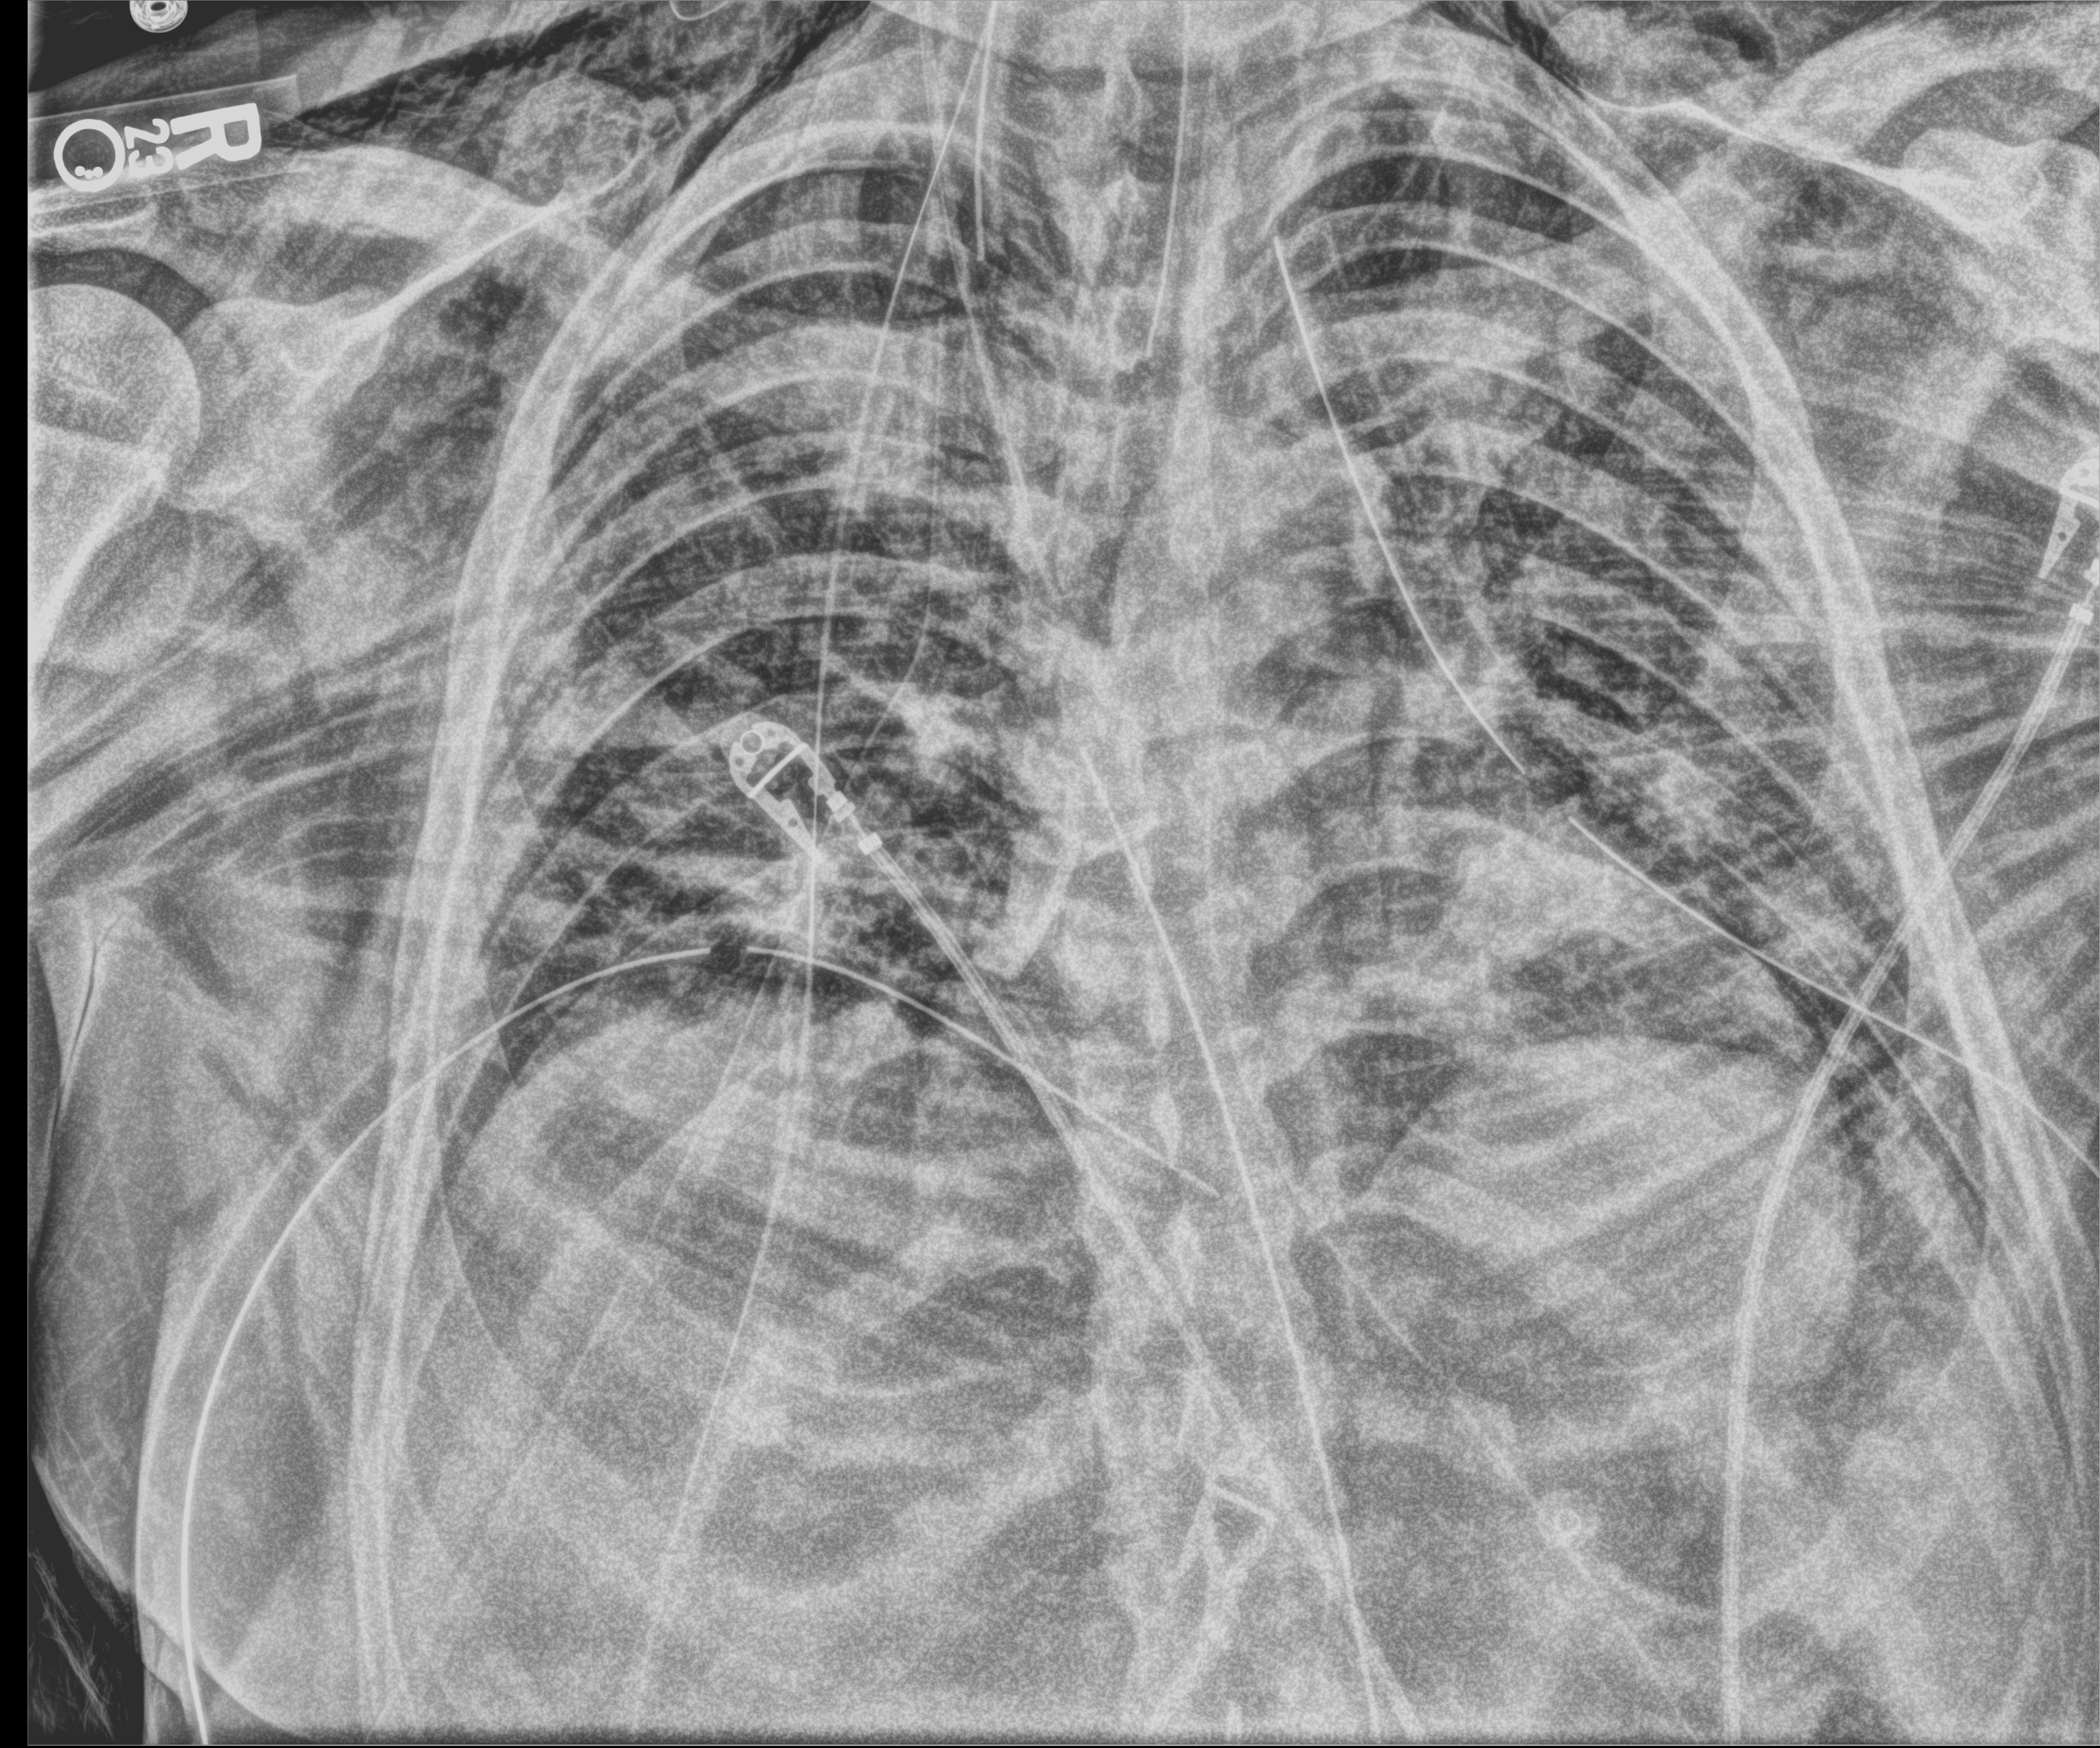
Bedside chest radiograph (computed radiography), anteroposterior (AP) projection. Male patient hospitalised with COVID-19, age 18–59 years.
Admission-level facts for this patient (not findings on this image; timing relative to this image not recorded): length of hospital stay: 29 days; mechanically ventilated during this hospital stay: yes.